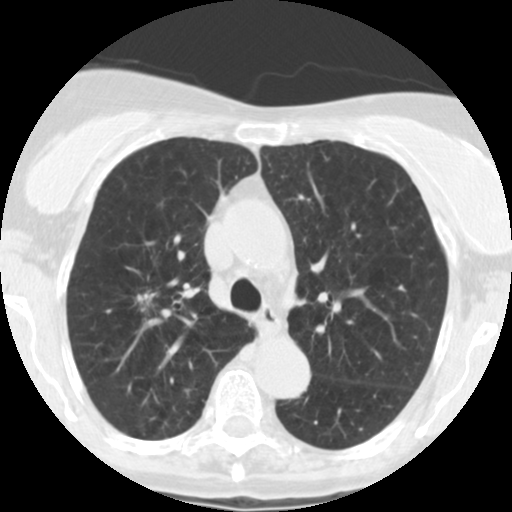
Low-dose screening chest CT, one axial slice. Position 171 of 246 along the scan axis. 120 kVp. Lung window (W 1500 / L -600 HU). 2.5 mm slice thickness. 512 × 512 image matrix, field of view 288 × 288 mm.
Annotated regions visible in this slice (expert manual segmentation):
- lesion 1 (tumor, upper lobe of right lung): box from (x=135, y=292) to (x=154, y=313) px